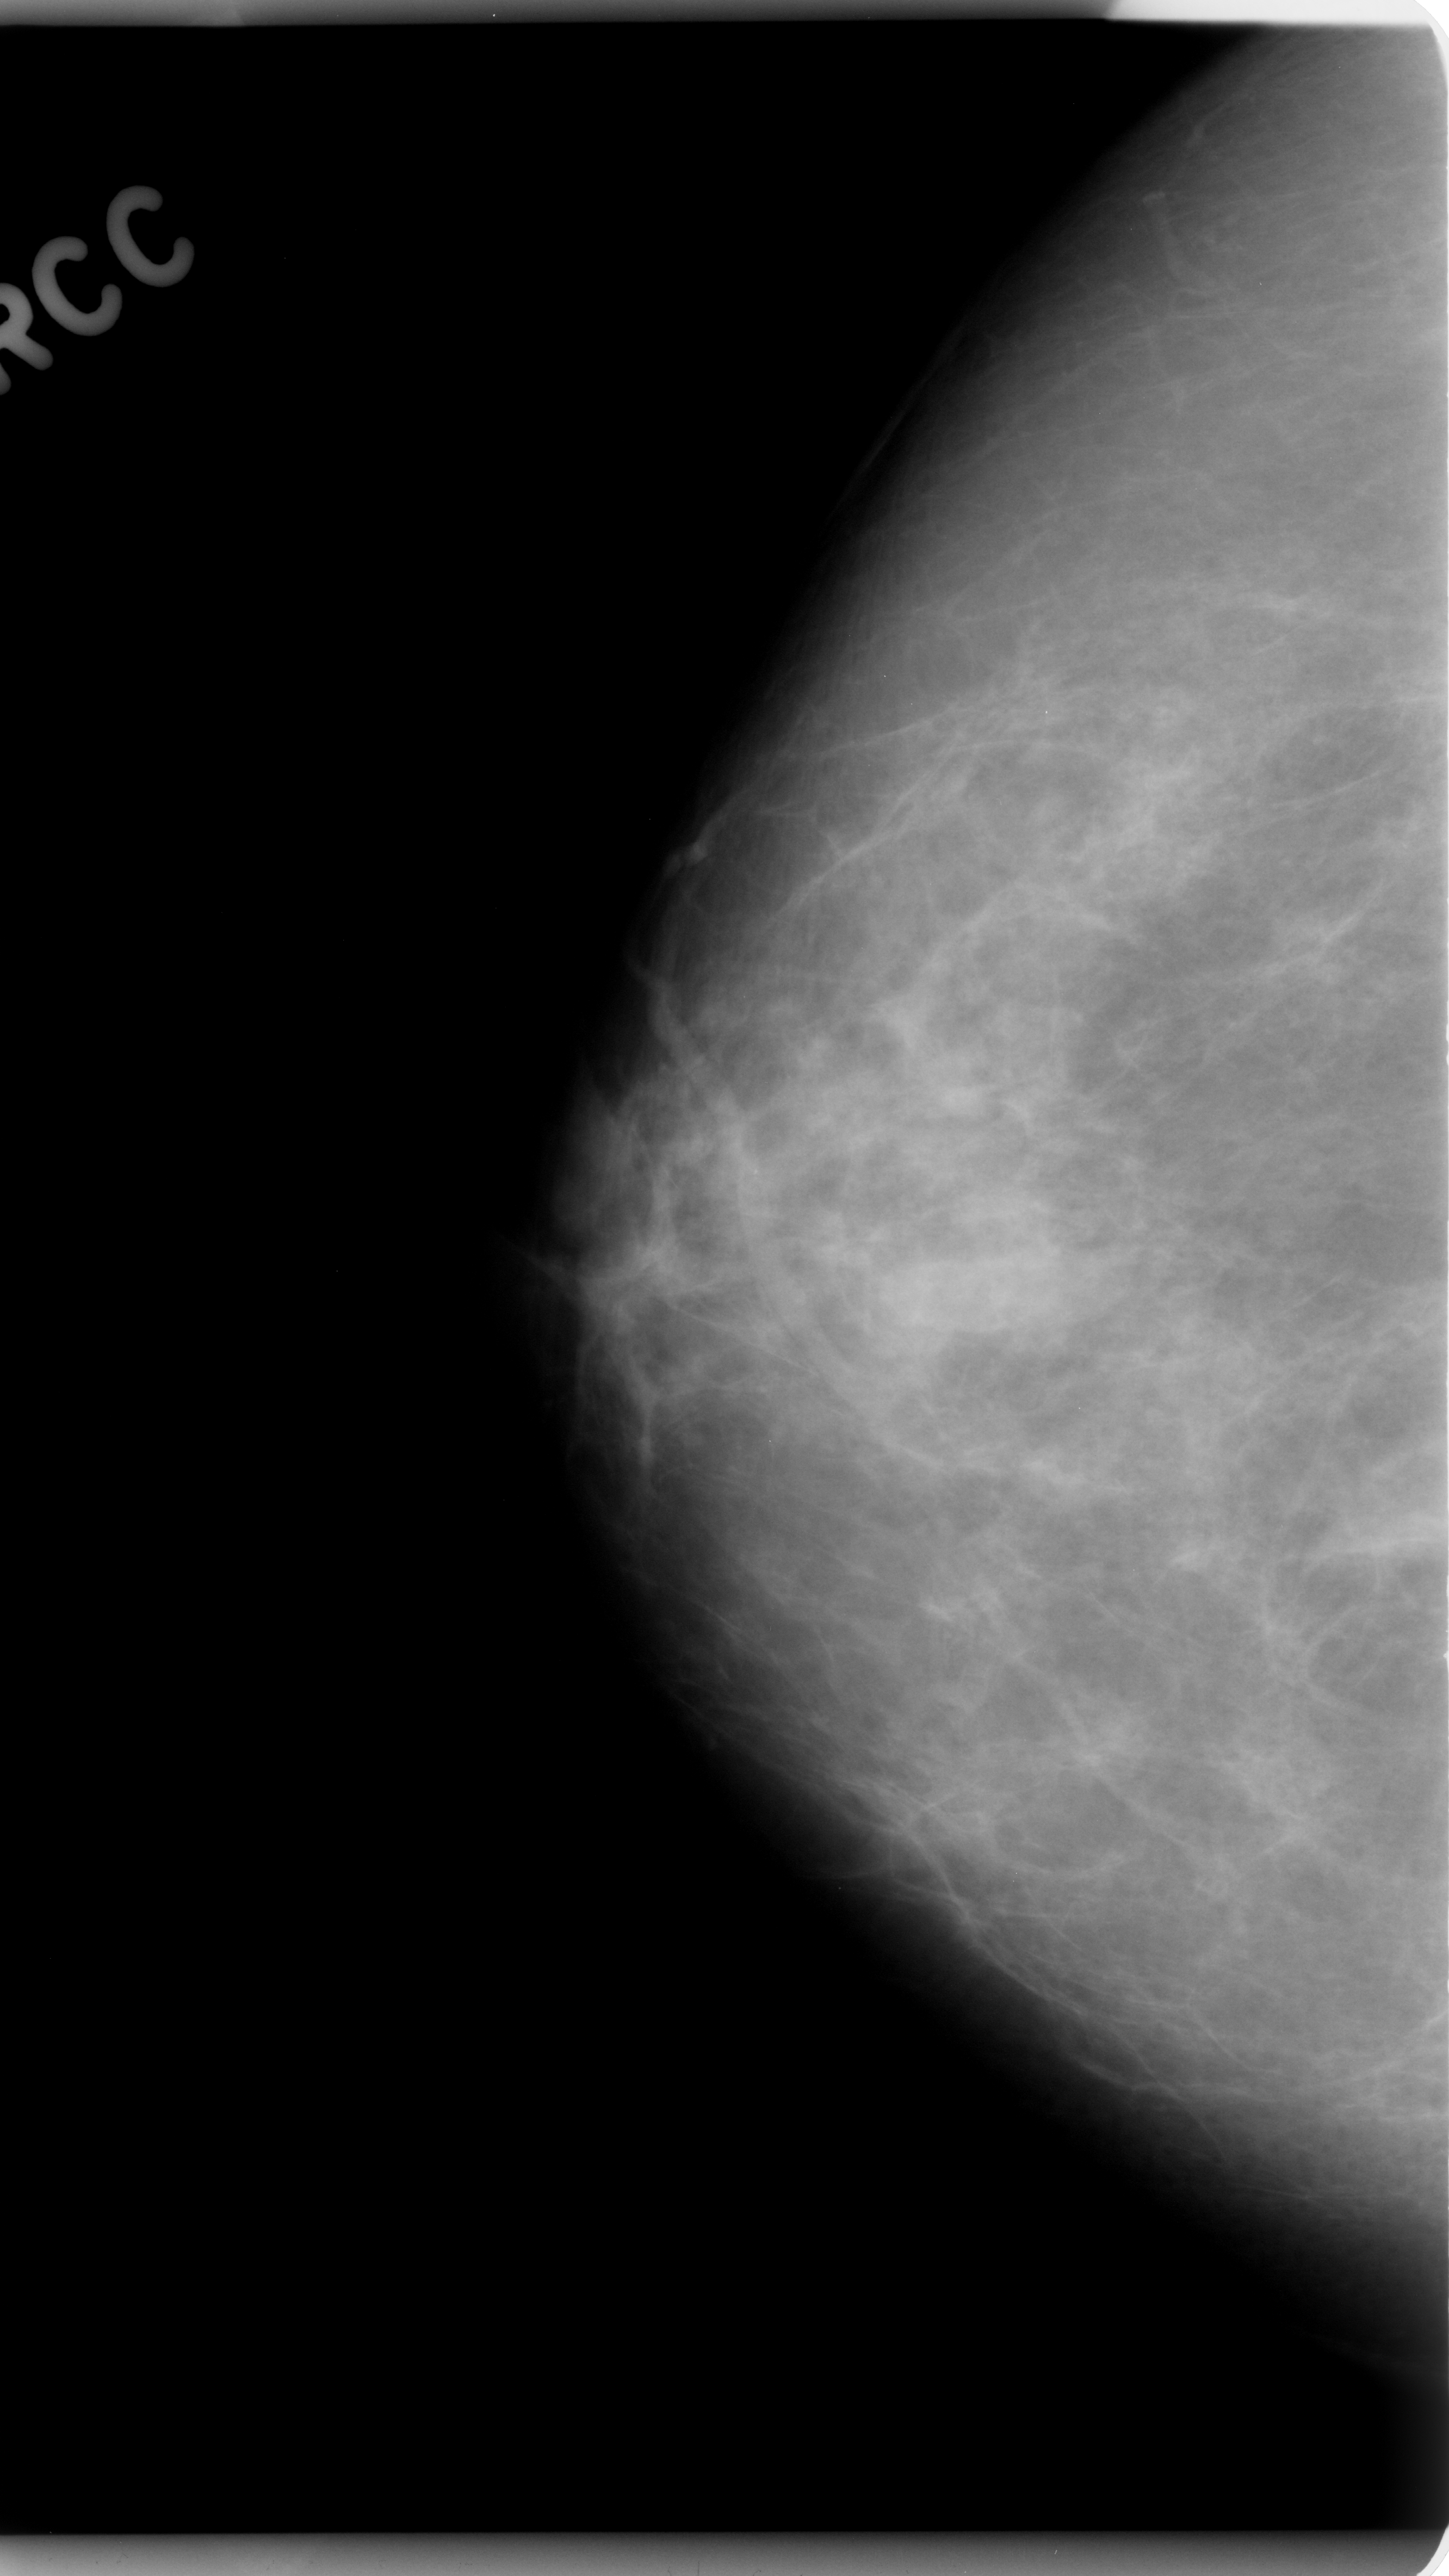
Mammogram (digitized film); right breast; CC view.
- Marked findings (only marked abnormalities are described; nothing is implied about the rest of the image): mass, shape irregular, margins ill defined; BI-RADS assessment category 4; pathology result (as recorded, not read from the image): benign.